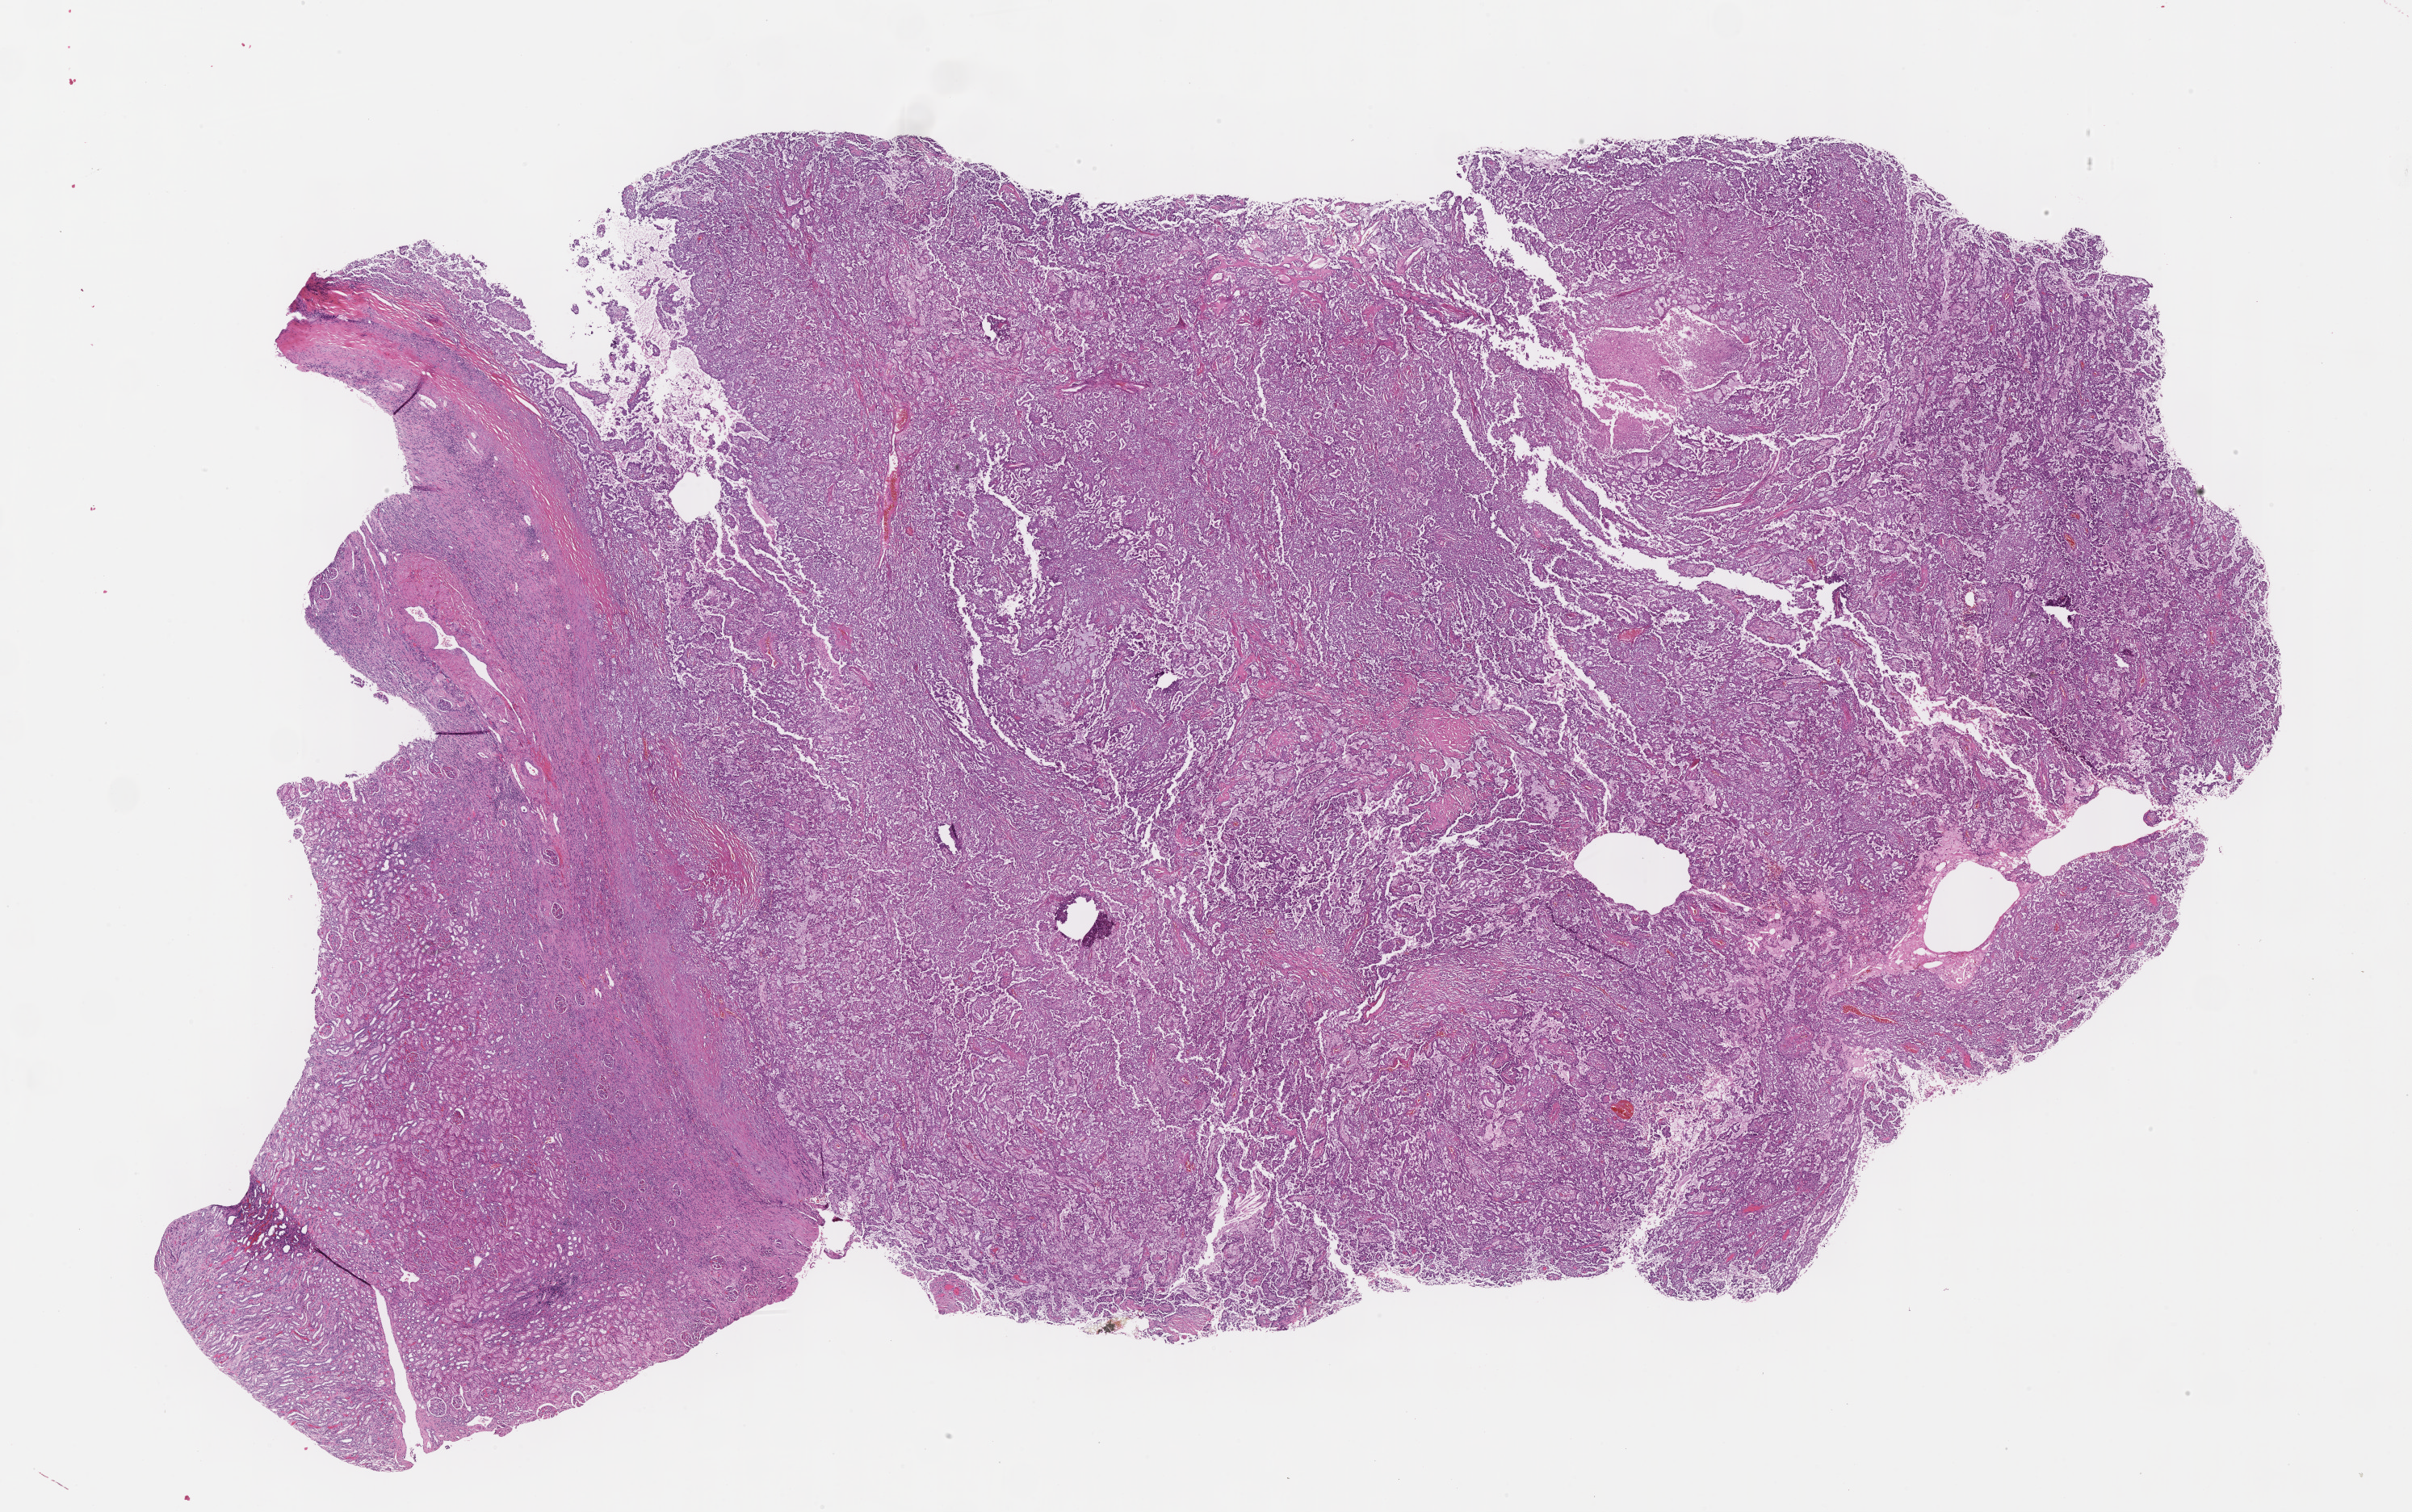
Digitized H&E tissue section (whole slide) — whole scanned area (about 24.2 x 15.1 mm) shown as a low-resolution overview; formalin-fixed paraffin-embedded (FFPE) diagnostic section; primary tumour sample from the kidney. Male, age 51 years at initial diagnosis.
Laterality: left. AJCC pathologic stage: I (7th edition). Diagnosis: Papillary adenocarcinoma, NOS.